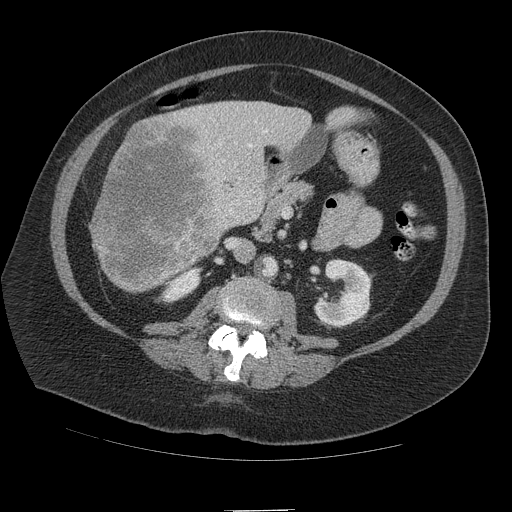
Contrast-enhanced abdominal CT (liver protocol), one axial slice. Position 42 of 109 along the scan axis. Reconstruction kernel STANDARD. 140 kVp. Soft-tissue window (W 400 / L 40 HU). 512 × 512 image matrix, field of view 420 × 420 mm. From the clinical record (not read from this slice): diagnosis: hepatocellular carcinoma (patient treated with transarterial chemoembolisation; whether this scan precedes or follows treatment is not stated here); TNM stage (as recorded): Stage-IVB; Child-Pugh class: A; tumour nodularity: multinodular.
Annotated regions visible in this slice (semi-automatically segmented with operator editing):
- liver parenchyma outside the tumour (the mass and vessels are separate outlines, so this box may not span the whole liver): bounding box [x1, y1, x2, y2] px = [92, 100, 358, 290]
- mass: [90, 113, 222, 293]
- liver vessels: [212, 129, 268, 213]